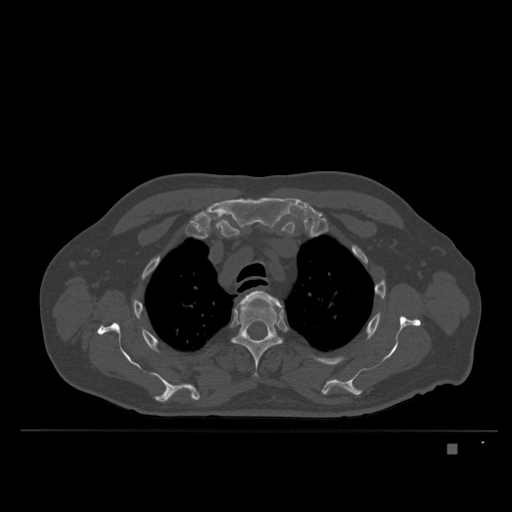
CT including the spine, one axial slice; slice 289 of 435 in the series (ordered by position); bone window (W 1800 / L 400 HU); 1.5 mm slice thickness; 512 × 512 image matrix, field of view 434 × 434 mm. Patient: male, 73 years. Case-level facts recorded for this patient, not image findings: primary cancer: skin.
Outlined on this slice (semi-automatic segmentation, software-assisted and operator-edited):
- T3 vertebra: bounding box <239,290,282,308> (left, top, right, bottom; pixels)
- T4 vertebra: <232,302,282,378>